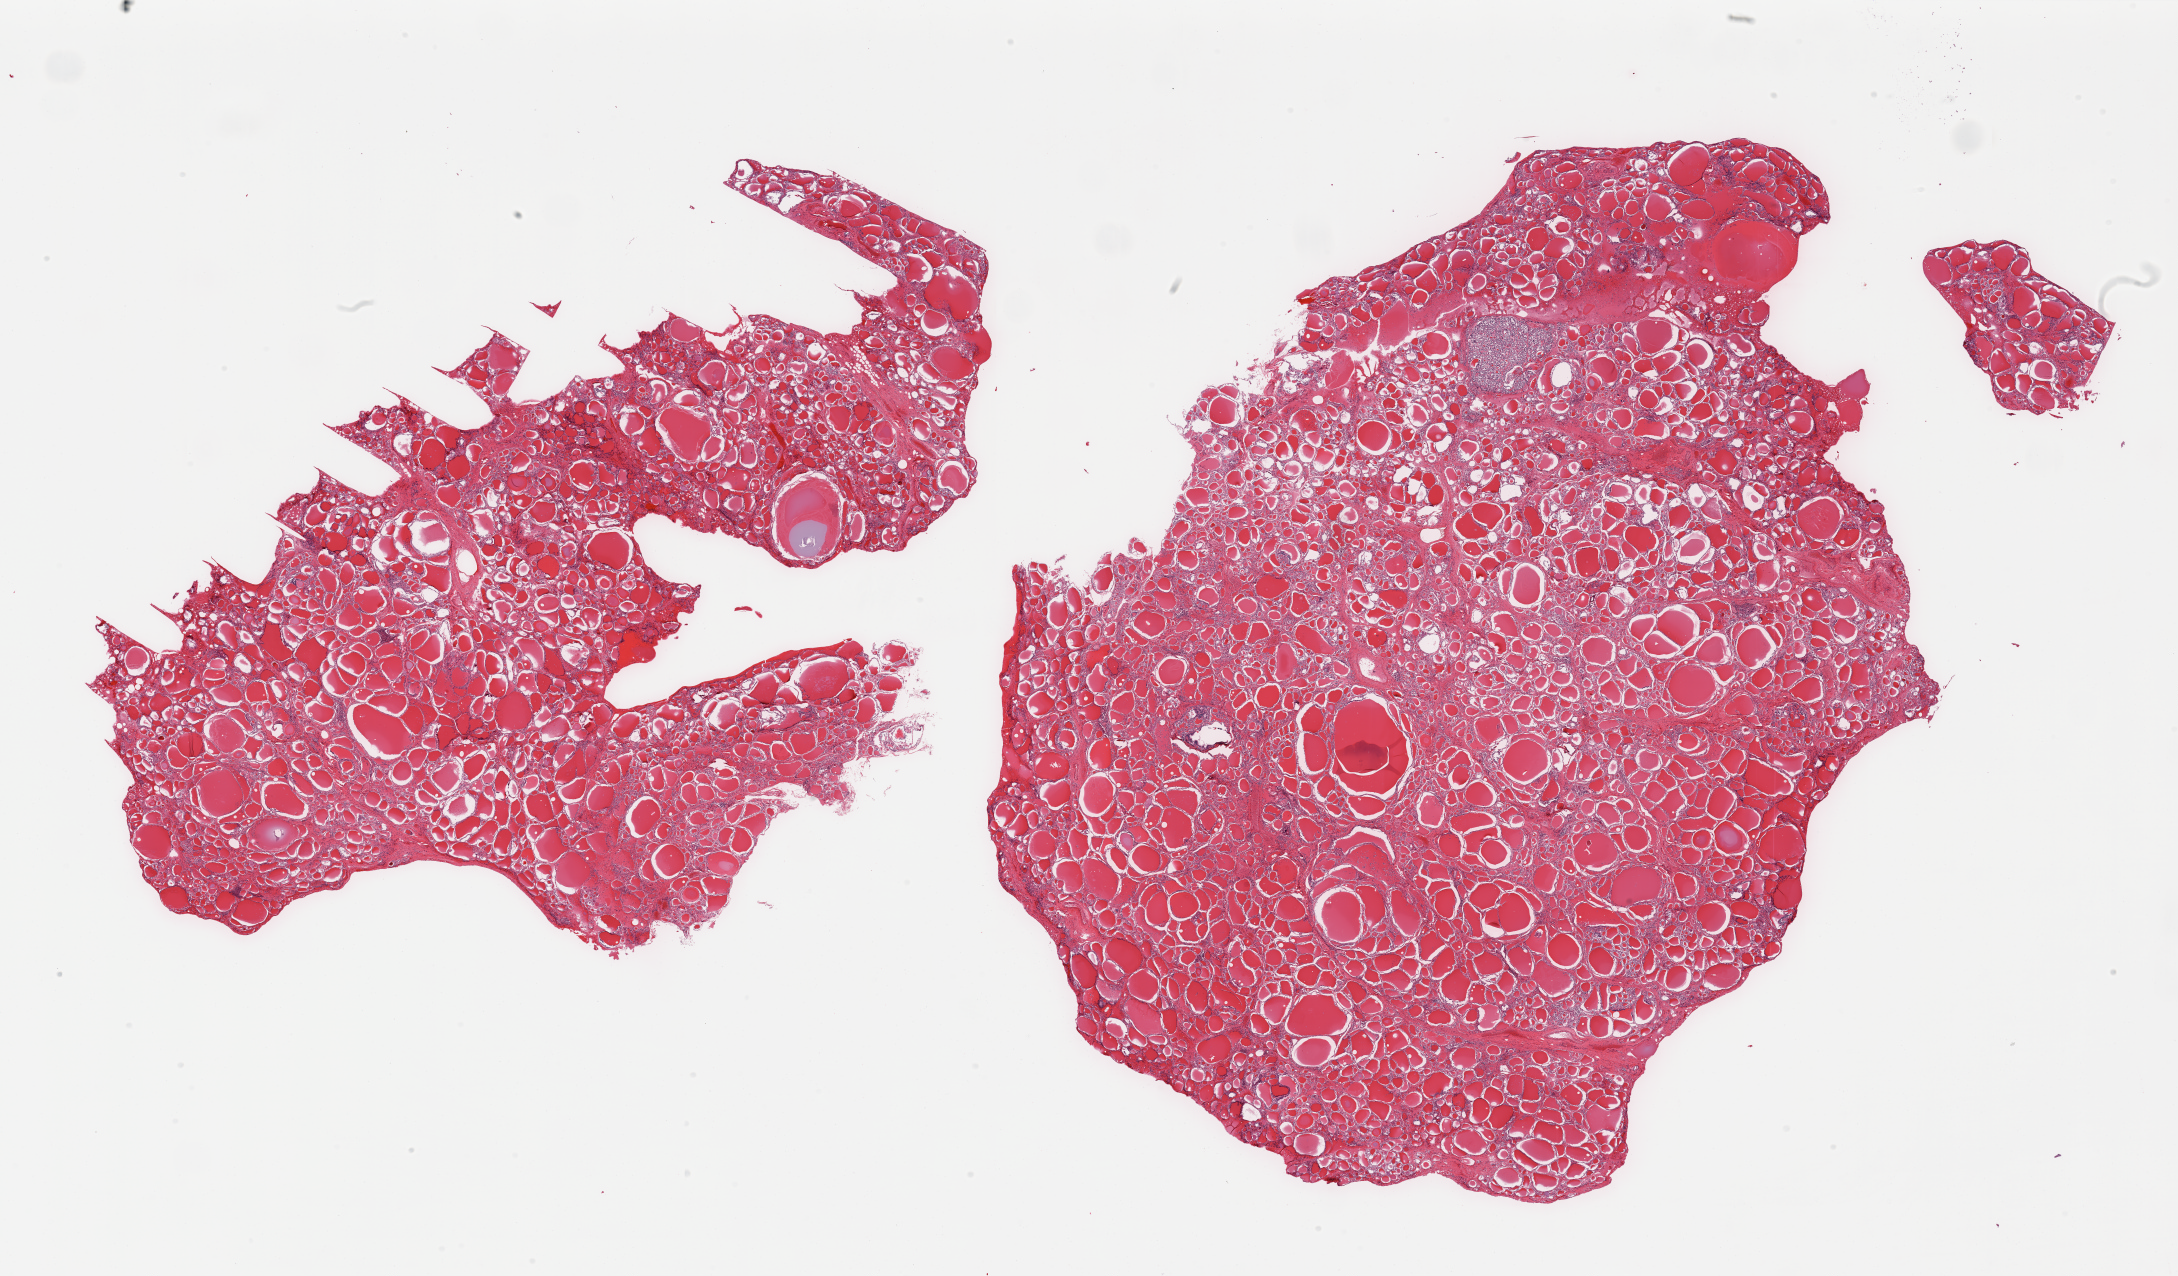
Digitized haematoxylin and eosin-stained section, brightfield — whole scanned area (about 34.5 x 20.2 mm) shown as a low-resolution overview, PAXgene-fixed, paraffin-embedded tissue, sampled site (target tissue): thyroid, donor tissue sample. Donor: male.
Review note (as recorded): 2 pieces; variation in size of thyroid follicles; one 1.27mm in diameter nodule.